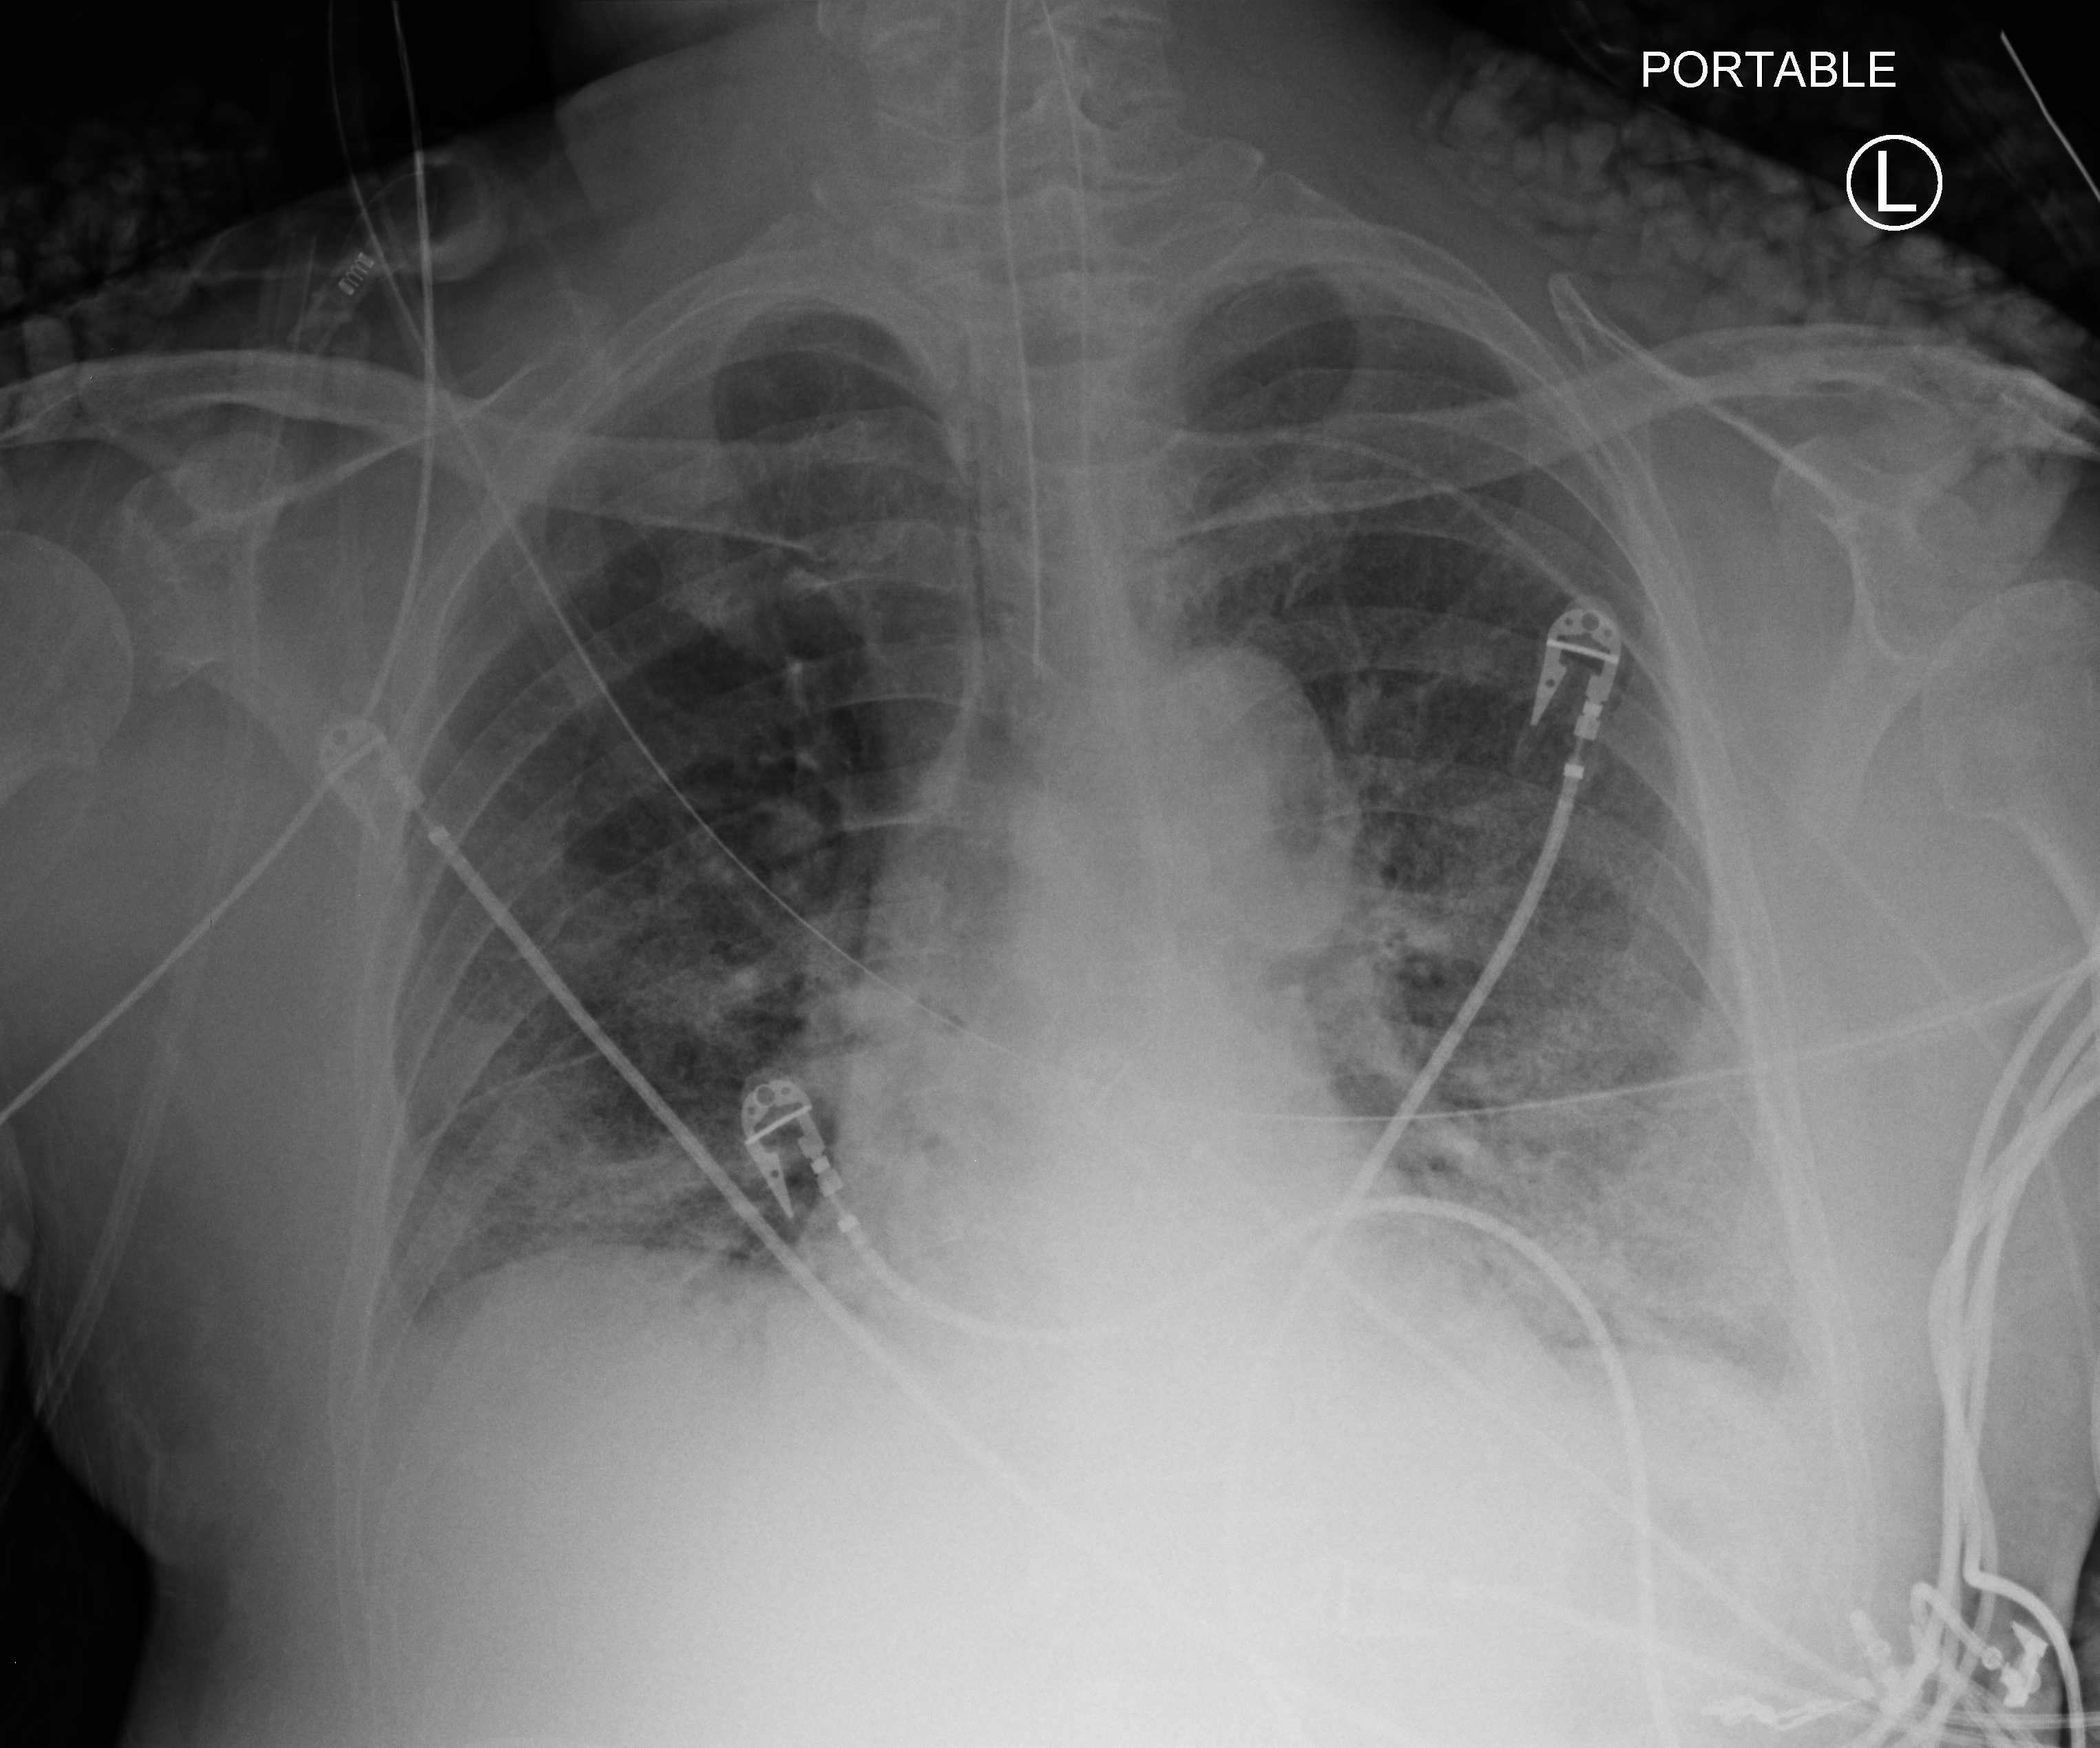
Portable chest radiograph, anteroposterior (AP) projection. Patient hospitalised with COVID-19; male, aged 60–74 years.
Admission-level facts for this patient (not findings on this image; timing relative to this image not recorded):
- COPD (admission record): no